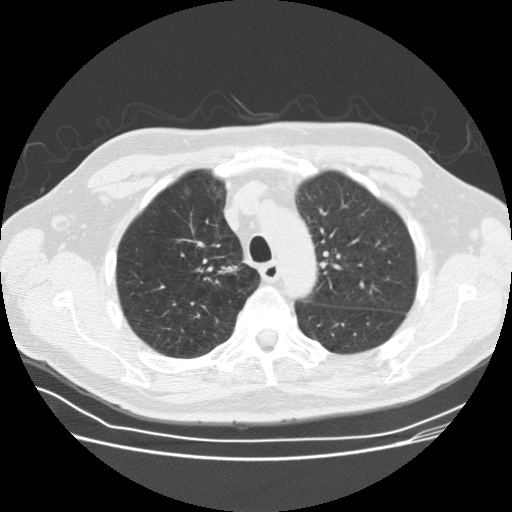
Chest CT (low-dose screening protocol), one axial image. Third annual screen. Lung window (W 1500 / L -600 HU). 2.5 mm slice thickness. 512 × 512 image matrix, field of view 360 × 360 mm. Male, age 69 years at enrolment. Current smoker at enrolment.
• Lesion marked by an expert reader, bounding box <221,256,260,288> (left, top, right, bottom; pixels).
• Reader record for this screening exam (exam-level; its link to the box is not recorded): non-calcified nodule or mass ≥4 mm, right upper lobe, 12 × 10 mm, spiculated (stellate) margins, soft tissue attenuation, pre-existing on the prior screen: yes; interval growth: yes.
• Official screen result: positive, other.
• Participant outcome: lung cancer diagnosed 36 days after this screen — squamous cell carcinoma, NOS, right upper lobe, moderately differentiated (G2), stage IA (AJCC 6th edition), 9 mm at pathology.